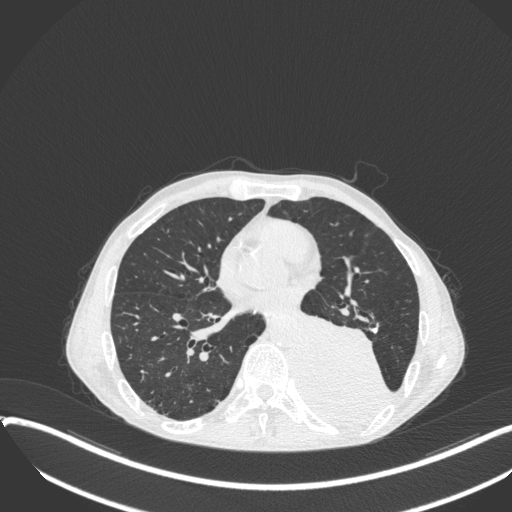
Chest CT, one axial slice; position 158 of 400 along the scan axis; reconstruction kernel B31f; 120 kVp; lung window (W 1500 / L -600 HU); 1 mm slice thickness; 512 × 512 image matrix. Patient: male, 57 years. Case-level facts recorded for this patient, not image findings: clinical TNM (as recorded): T4 N0 M0.
Outlined on this slice (rectangle marked by the reading radiologist):
- lung tumour (recorded histology: squamous cell carcinoma): box from (x=297, y=310) to (x=394, y=431) px